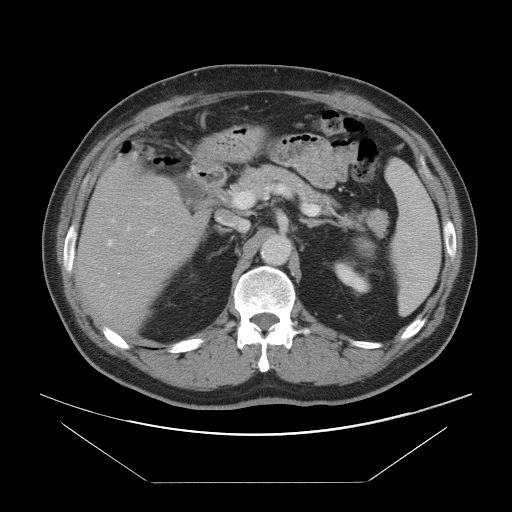
Contrast-enhanced abdominal CT, one axial slice; slice 51 of 97 in the series (ordered by position); intravenous contrast given; soft-tissue window (W 400 / L 40 HU); 512 × 512 image matrix, field of view 442 × 442 mm. Male patient, age 62 years. Case-level facts recorded for this patient, not image findings: diagnosis: colorectal cancer liver metastases, imaged before liver resection; multiple liver metastases: no; largest metastasis: 7 cm; disease in both lobes: yes.
Structures marked on this image (outlined manually by an expert reader):
- hepatic veins: box from (x=108, y=225) to (x=175, y=258) px
- liver: (x=77, y=158)–(x=198, y=333)
- planned liver remnant (the part of the liver to remain after resection): (x=77, y=174)–(x=199, y=334)
- portal vein (with intrahepatic branches): (x=111, y=203)–(x=157, y=234)